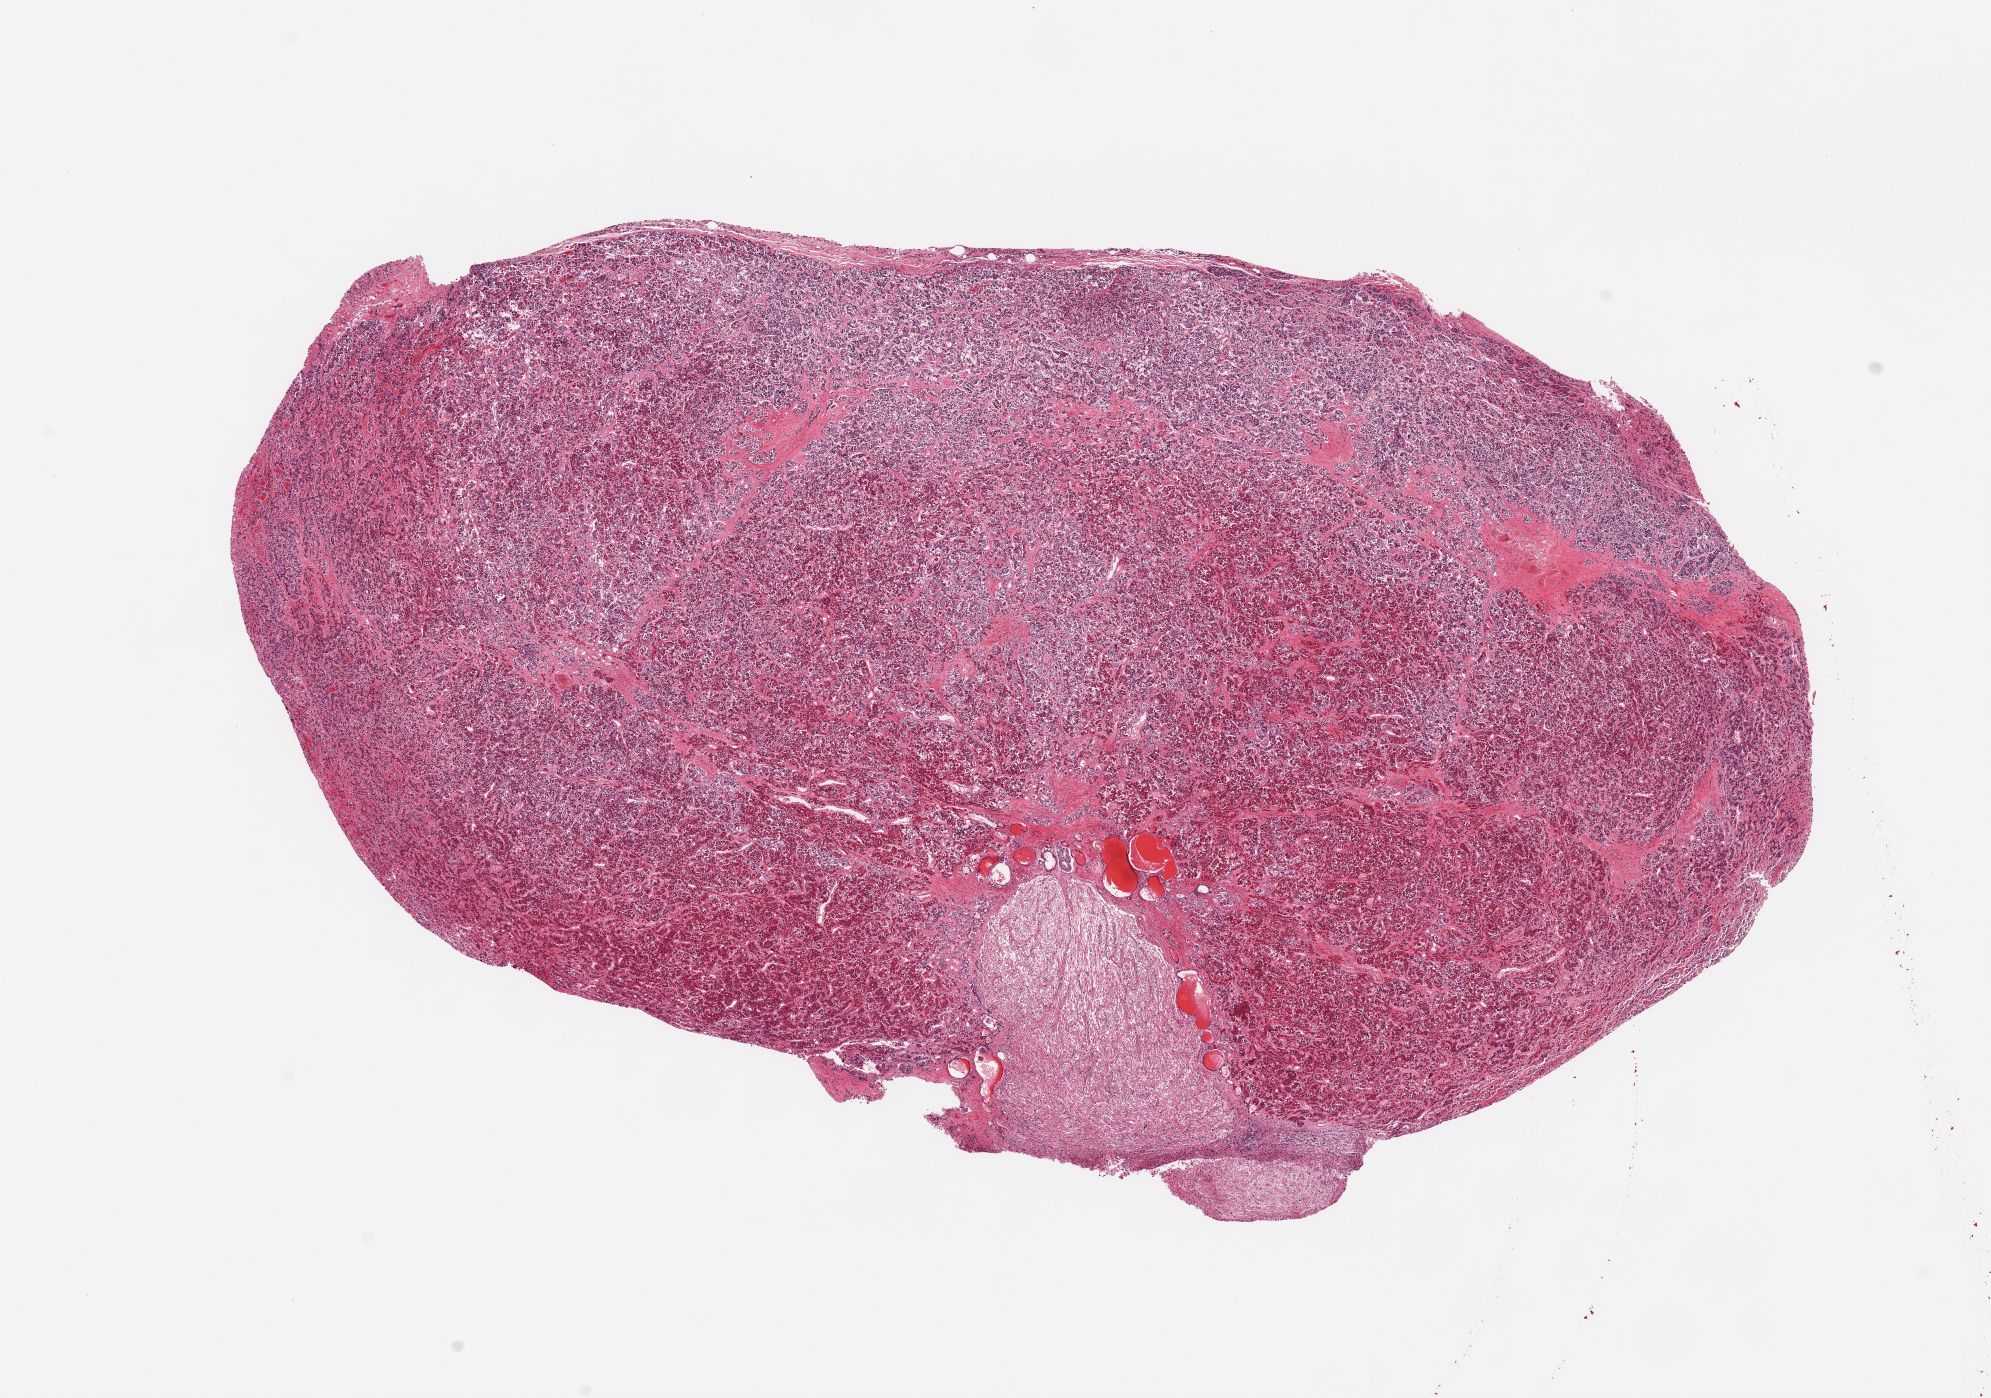
Haematoxylin and eosin whole-slide image — a low-resolution overview of the entire scanned area, about 15.8 x 11.1 mm; PAXgene-fixed paraffin-embedded (PFPE) section; sampled site (target tissue): pituitary; tissue donor sample. Male donor.
• reviewer comment on this tissue sample: 1 piece, mainly adenohypophysis; 3x2mm focus of neurohypophysis